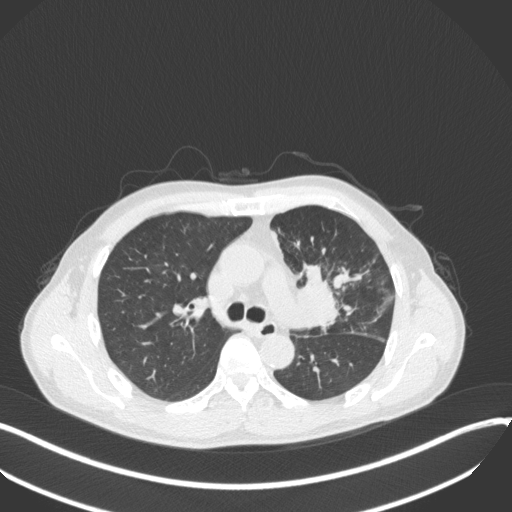
Chest CT, one axial slice; reconstruction kernel B31f; 120 kVp; lung window (W 1500 / L -600 HU); 512 × 512 image matrix, field of view 400 × 400 mm. Male patient, age 56 years. Case-level facts recorded for this patient, not image findings: clinical TNM (as recorded): T2a N0 M0.
Annotated regions visible in this slice (bounding box drawn by a radiologist):
- lung tumour (recorded histology: squamous cell carcinoma): bounding box (x1, y1, x2, y2) in pixels: (294, 261, 345, 336)